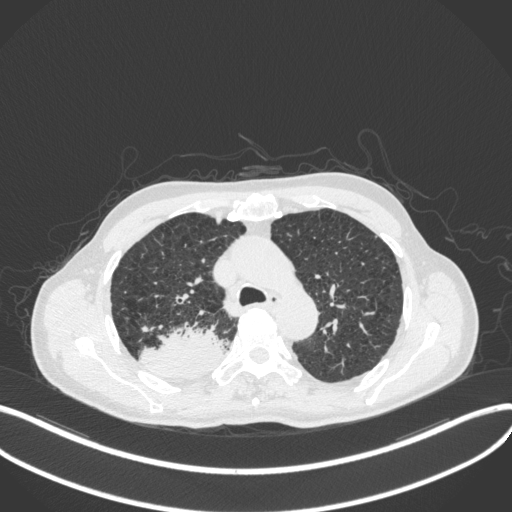
Chest CT, one axial slice; slice 322 of 423 in the series (ordered by position); reconstruction kernel B31f; 120 kVp; lung window (W 1500 / L -600 HU); 512 × 512 image matrix, field of view 400 × 400 mm. Patient: male, 79 years. Case-level facts recorded for this patient, not image findings: clinical TNM (as recorded): T3 N0 M0.
Annotated regions visible in this slice (bounding box drawn by a radiologist):
- lung tumour (recorded histology: adenocarcinoma): bounding box (x1, y1, x2, y2) in pixels: (137, 325, 225, 383)